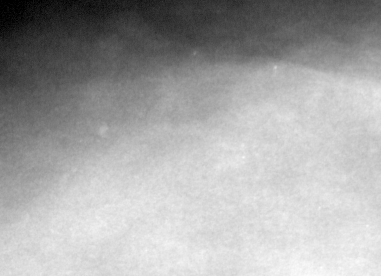
Cropped region of a digitized screen-film mammogram centred on a radiologist-marked abnormality, left breast, CC view, BI-RADS breast density category 4 (scale 1–4).
Calcifications, morphology pleomorphic, distribution clustered; BI-RADS assessment category 4; subtlety rating 1 on a 1 (subtle) to 5 (obvious) scale; pathology (as recorded): malignant.